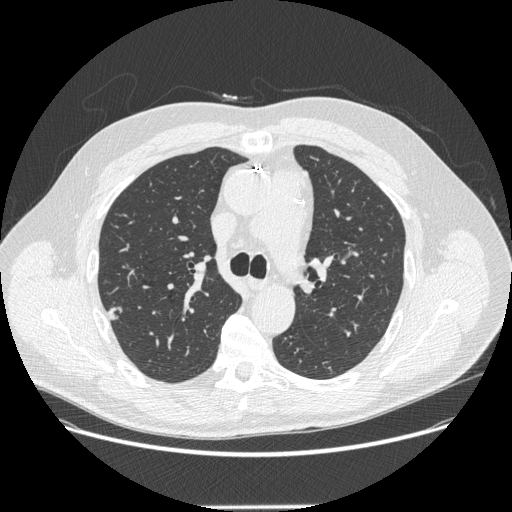
Low-dose screening chest CT, one axial slice. Position 188 of 265 along the scan axis. Reconstruction kernel STANDARD. 120 kVp. Lung window (W 1500 / L -600 HU). 512 × 512 image matrix, field of view 400 × 400 mm.
Structures marked on this image (expert manual segmentation):
- lesion 1 (tumor, upper lobe of right lung): bounding box [x1, y1, x2, y2] px = [107, 307, 123, 320]